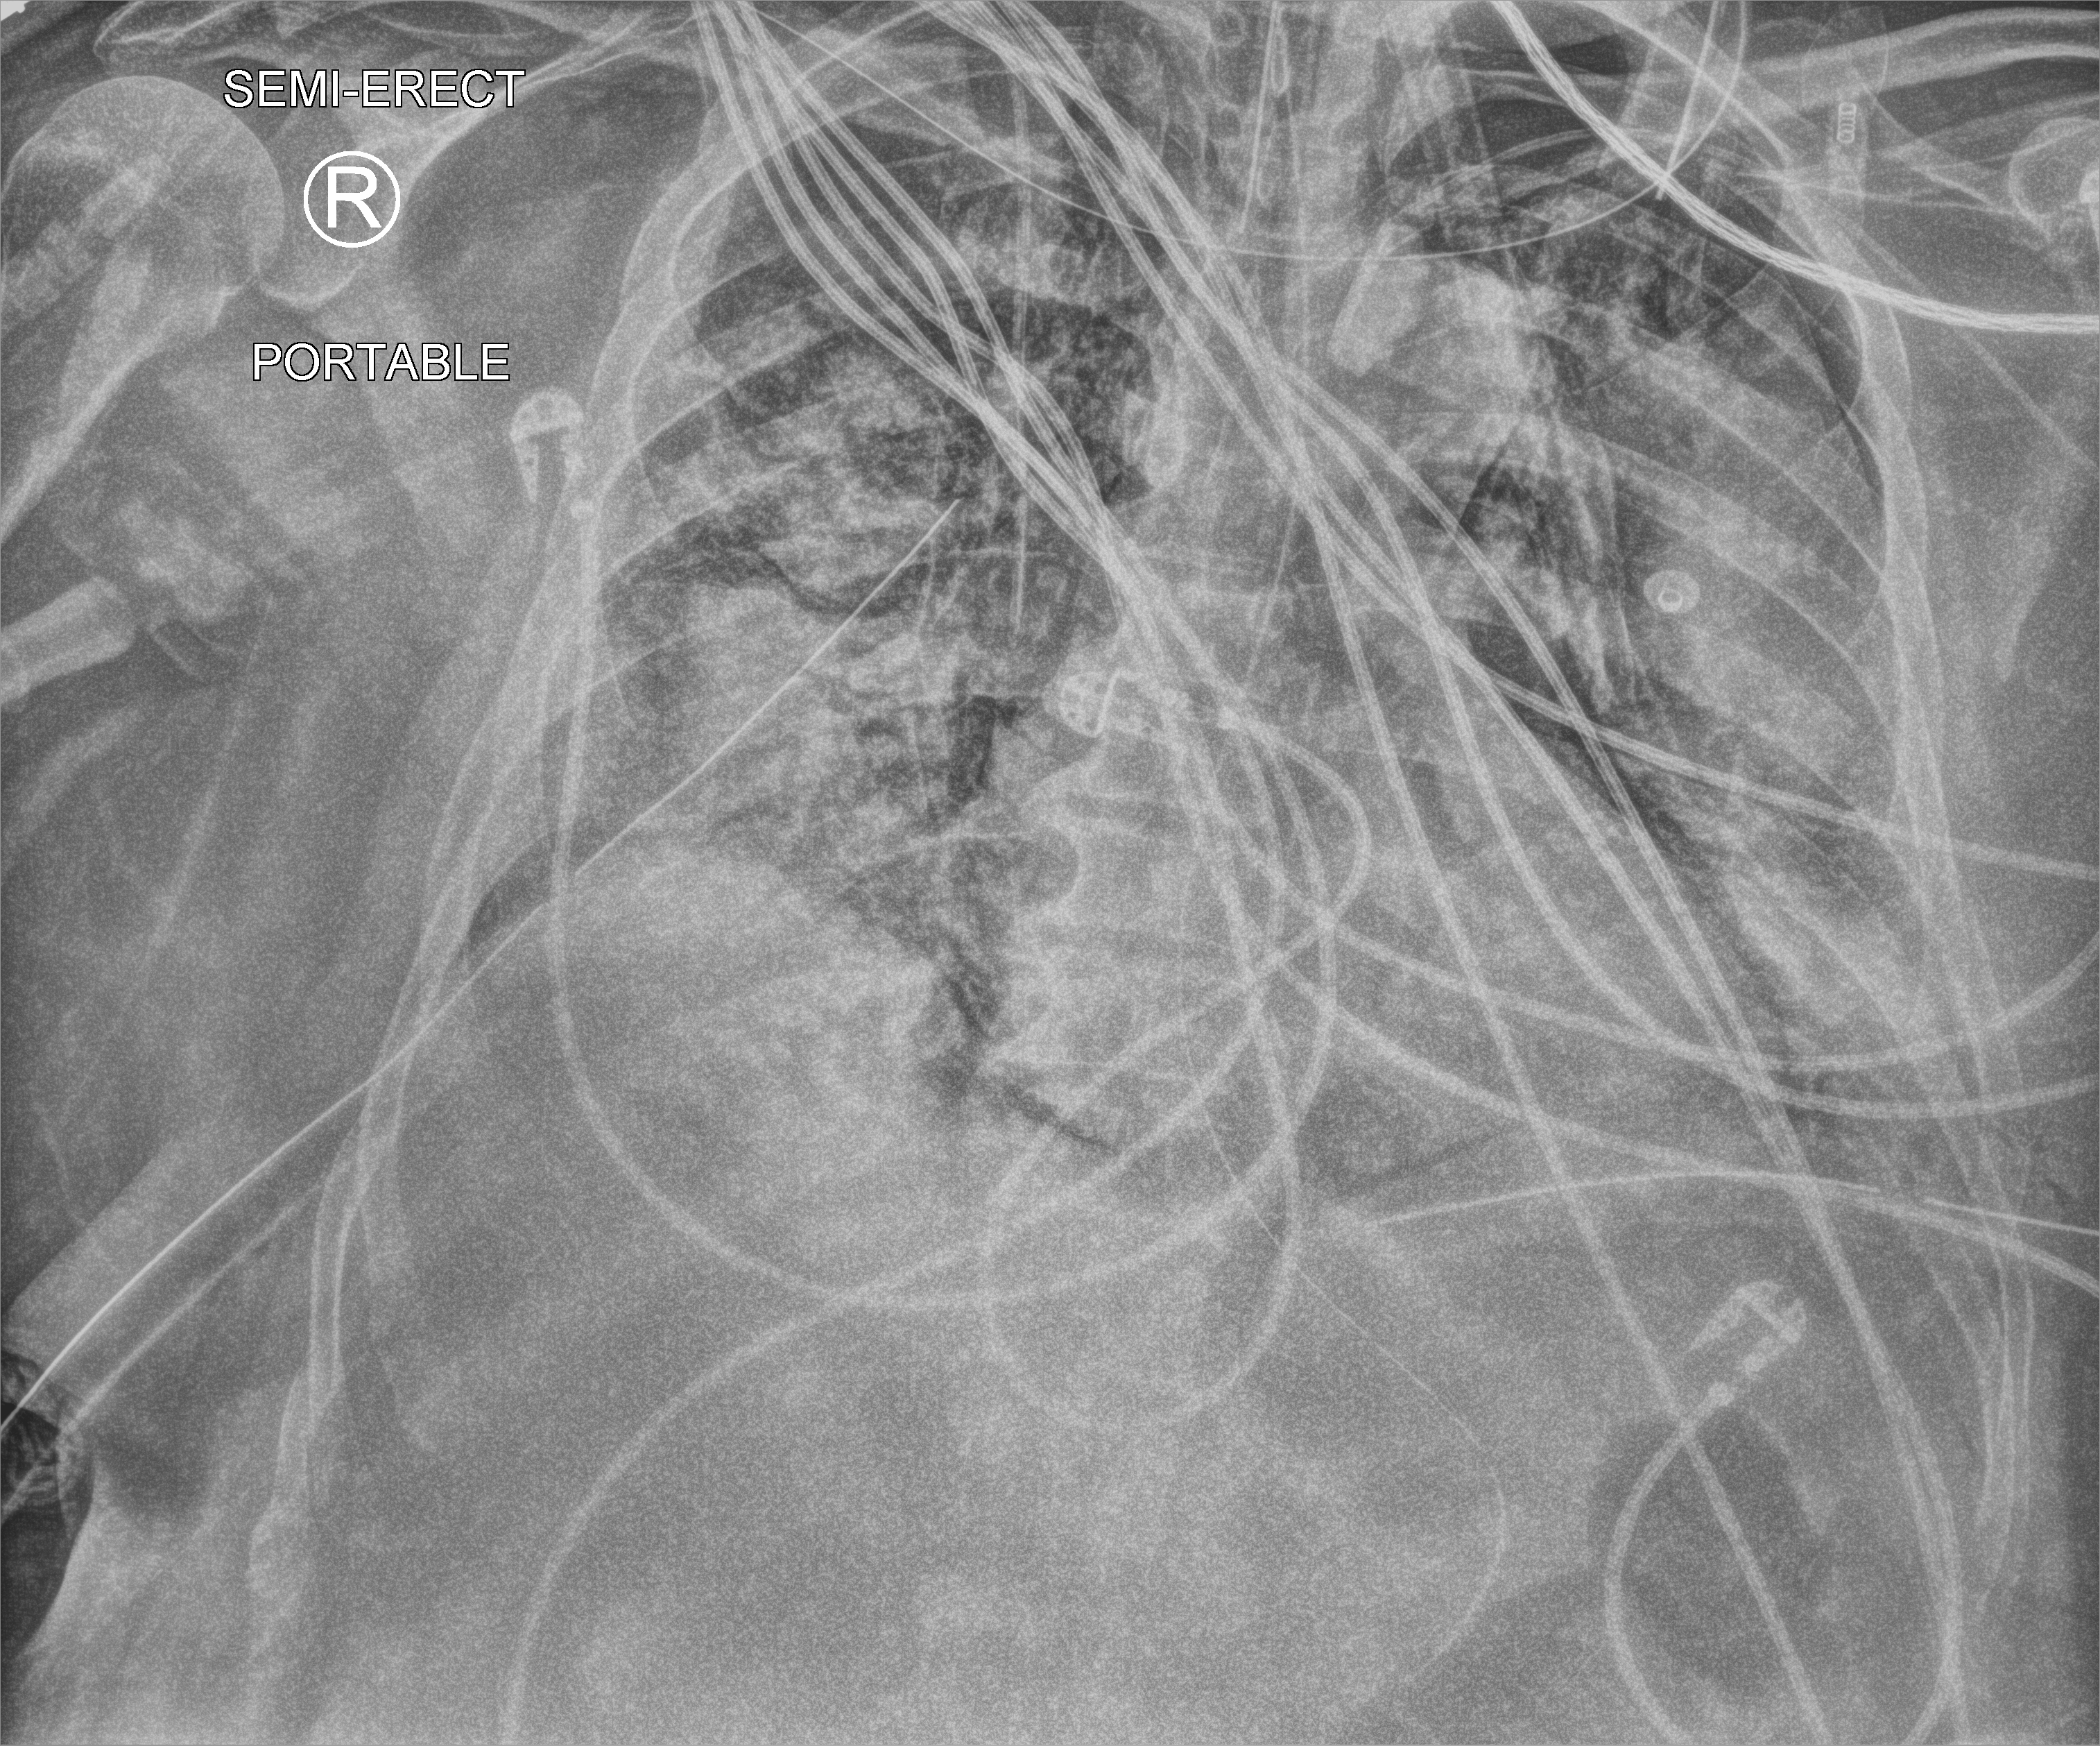
Chest X-ray (portable); anteroposterior (AP) projection. Patient hospitalised with COVID-19, aged 18–59 years.
Admission-level facts for this patient (not findings on this image; timing relative to this image not recorded):
- mechanically ventilated during this hospital stay: yes